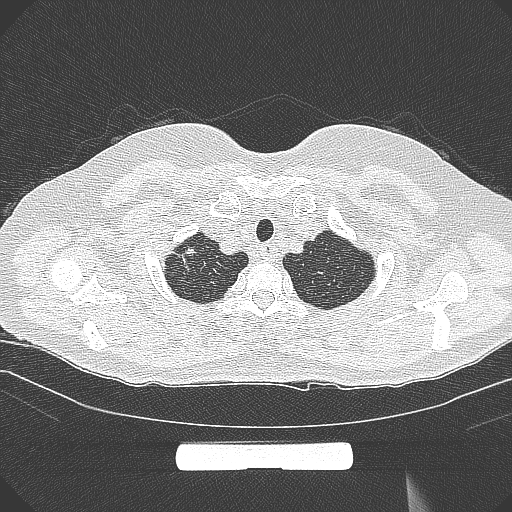
Chest CT, one axial slice. Position 266 of 295 along the scan axis. 120 kVp. Lung window (W 1500 / L -600 HU). 1 mm slice thickness. 512 × 512 image matrix, field of view 369 × 369 mm. Female patient, age 58 years. Case-level facts recorded for this patient, not image findings: clinical TNM (as recorded): T1b N0 M0.
Outlined on this slice (rectangle marked by the reading radiologist):
- lung tumour (recorded histology: adenocarcinoma): bounding box <174,242,206,283> (left, top, right, bottom; pixels)